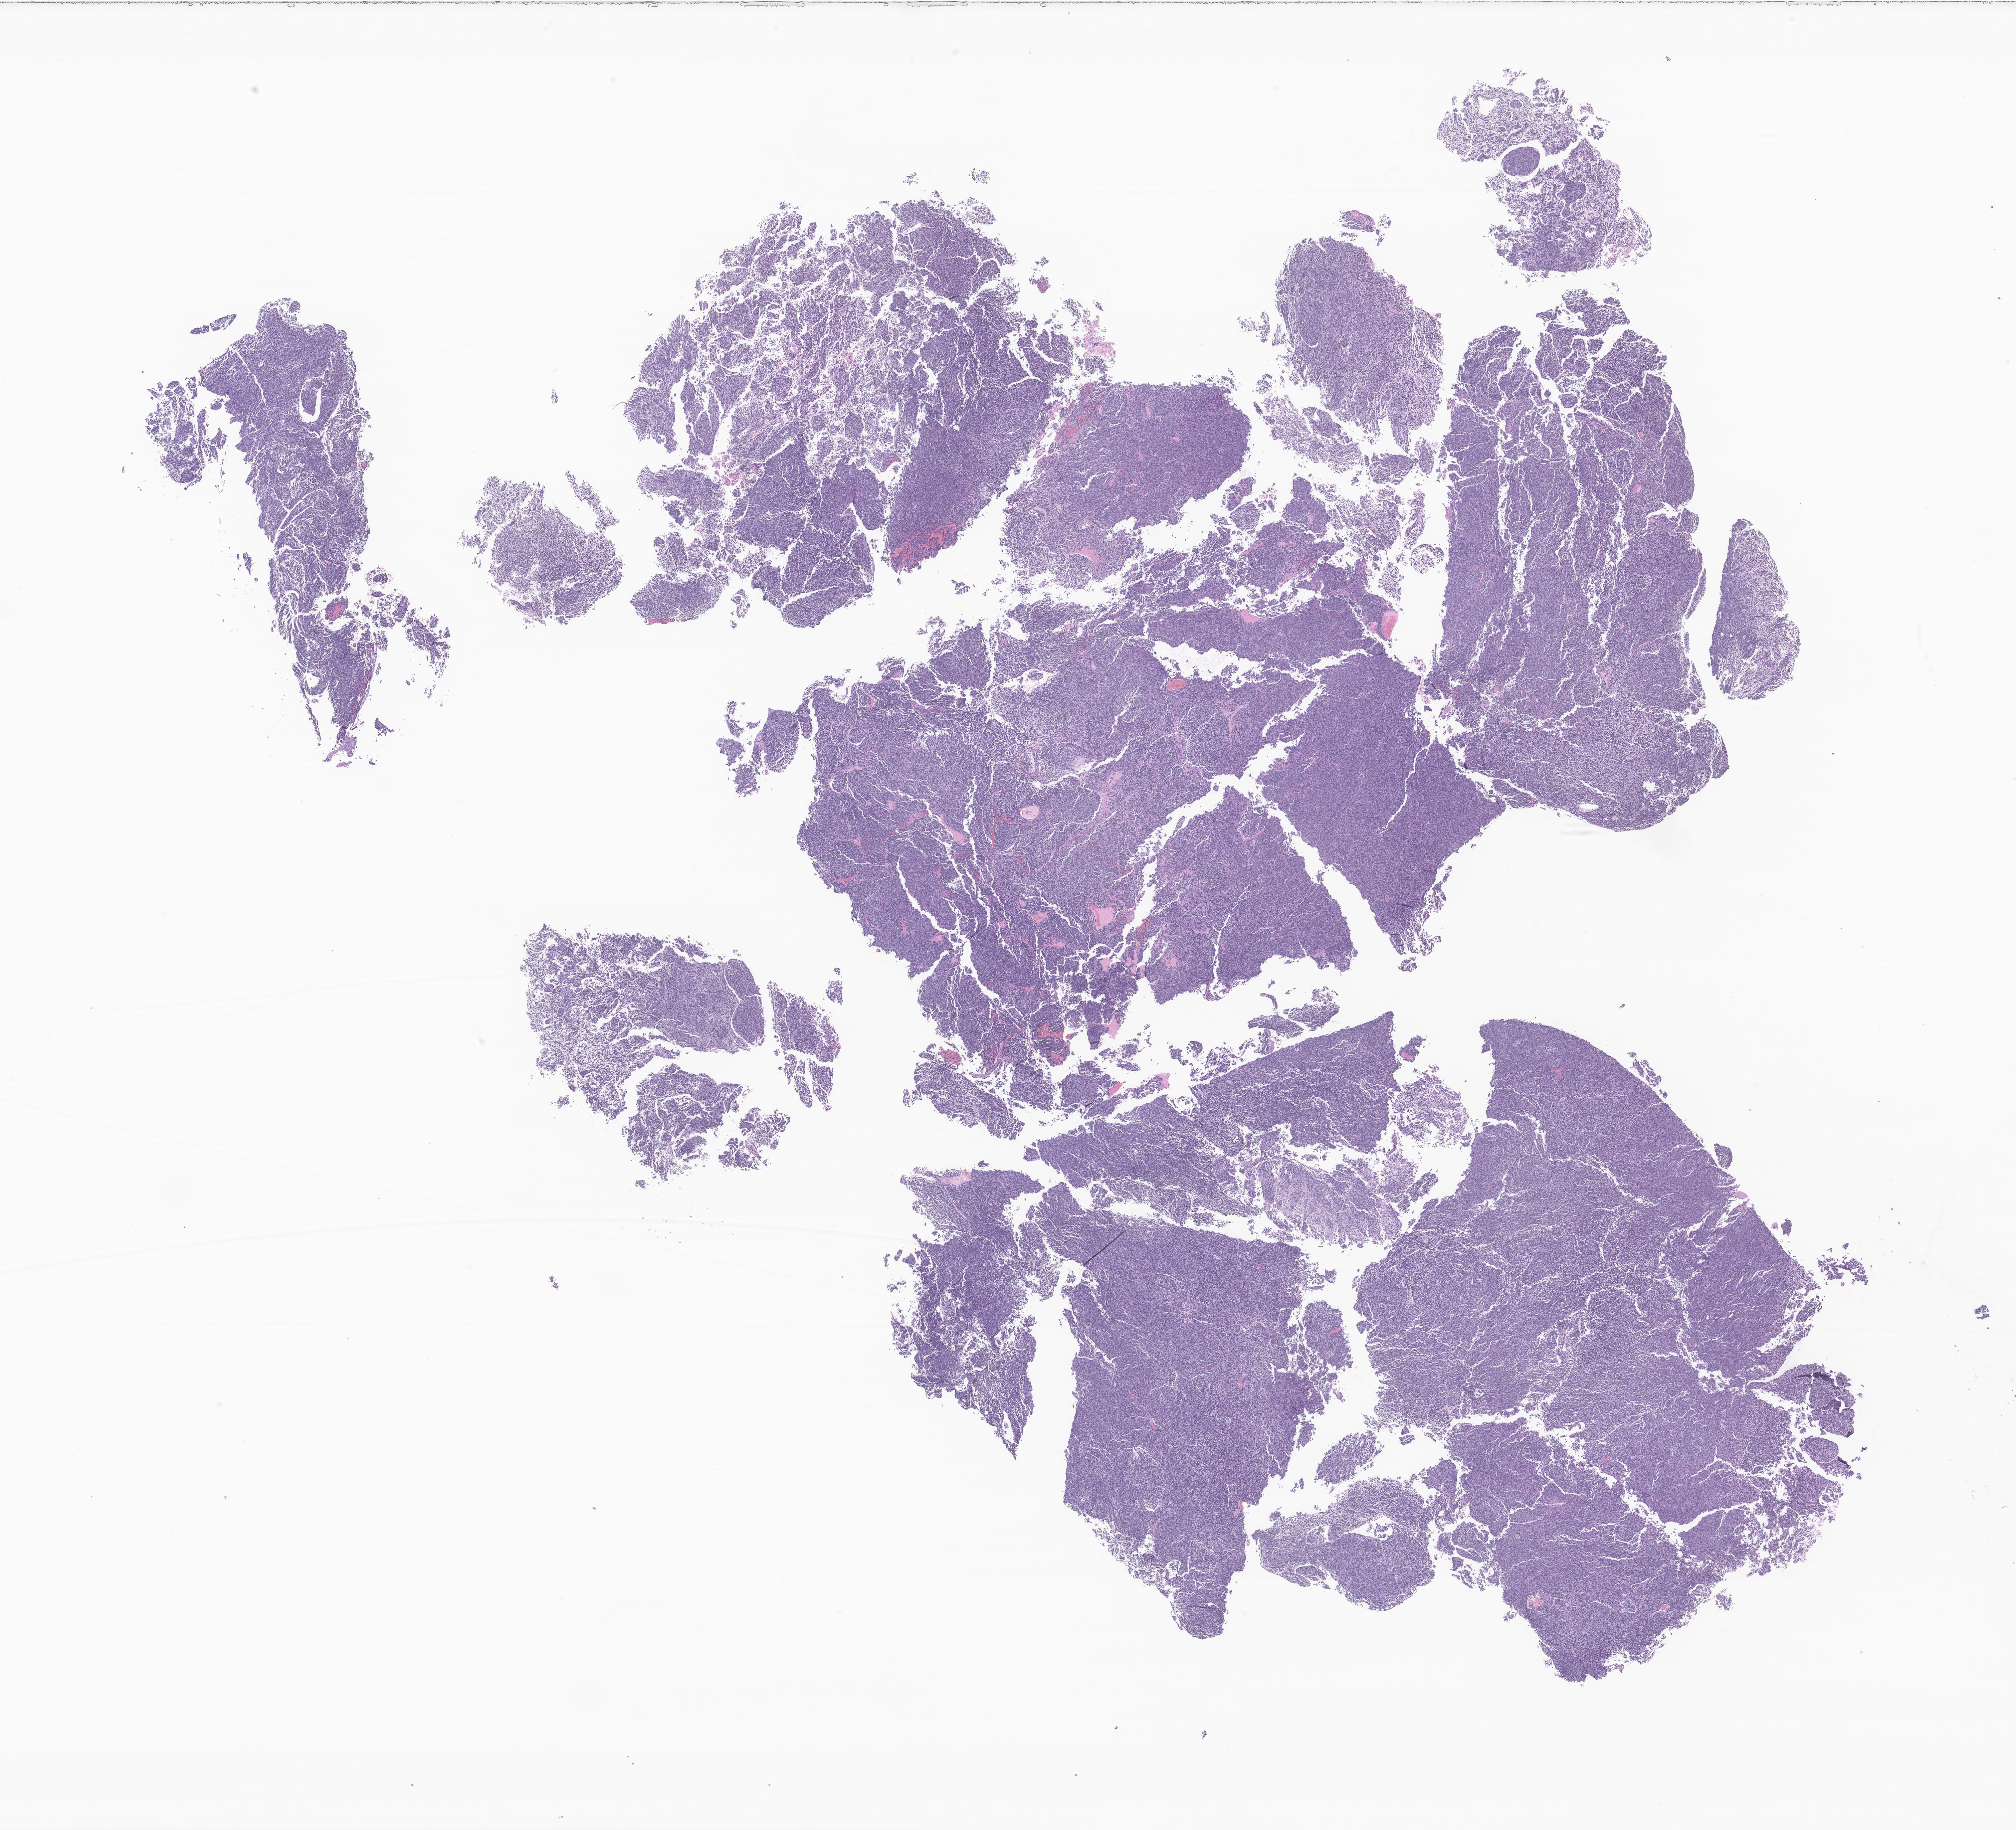
H&E whole-slide image of tumor tissue from the cerebellum, low-resolution overview of the scanned area, about 25.5 x 23.2 mm. FFPE section. Patient female; age 274 months (22 years 10 months).
Diagnosis (ICD-O-3 morphology term): Medulloblastoma, NOS.